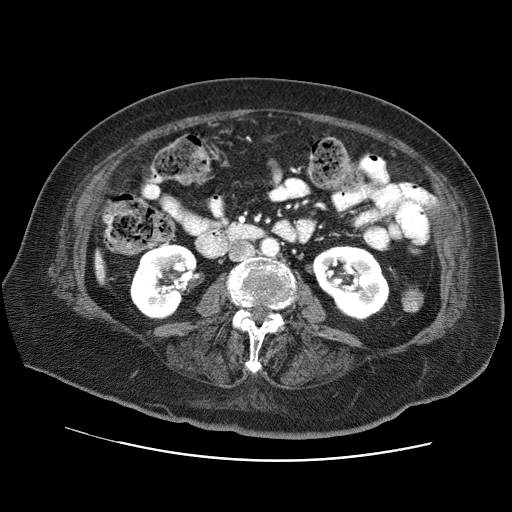
Contrast-enhanced abdominal CT (liver protocol), one axial slice; 120 kVp; soft-tissue window (W 400 / L 40 HU); 2.5 mm slice thickness; 512 × 512 image matrix, field of view 380 × 380 mm. From the clinical record (not read from this slice): diagnosis: hepatocellular carcinoma (patient treated with transarterial chemoembolisation; whether this scan precedes or follows treatment is not stated here); TNM stage (as recorded): Stage-I; Child-Pugh class: A; tumour nodularity: uninodular.
Outlined on this slice (semi-automatically segmented with operator editing):
- liver parenchyma outside the tumour (the mass and vessels are separate outlines, so this box may not span the whole liver): bounding box [x1, y1, x2, y2] px = [94, 250, 104, 283]